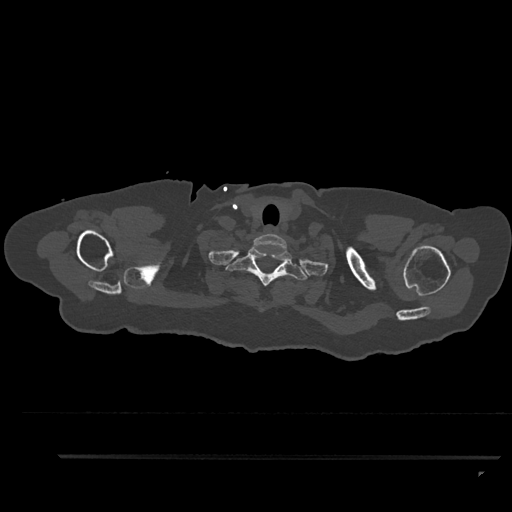
CT including the spine, one axial slice; position 769 of 797 along the scan axis; reconstruction kernel Br40s/3; 120 kVp; bone window (W 1800 / L 400 HU); 0.5 mm slice thickness; 512 × 512 image matrix, field of view 408 × 408 mm. Patient: female, 44 years. Case-level facts recorded for this patient, not image findings: primary cancer: renal.
Annotated regions visible in this slice (semi-automatic segmentation, software-assisted and operator-edited):
- T1 vertebra: bounding box [x1, y1, x2, y2] px = [225, 246, 309, 286]